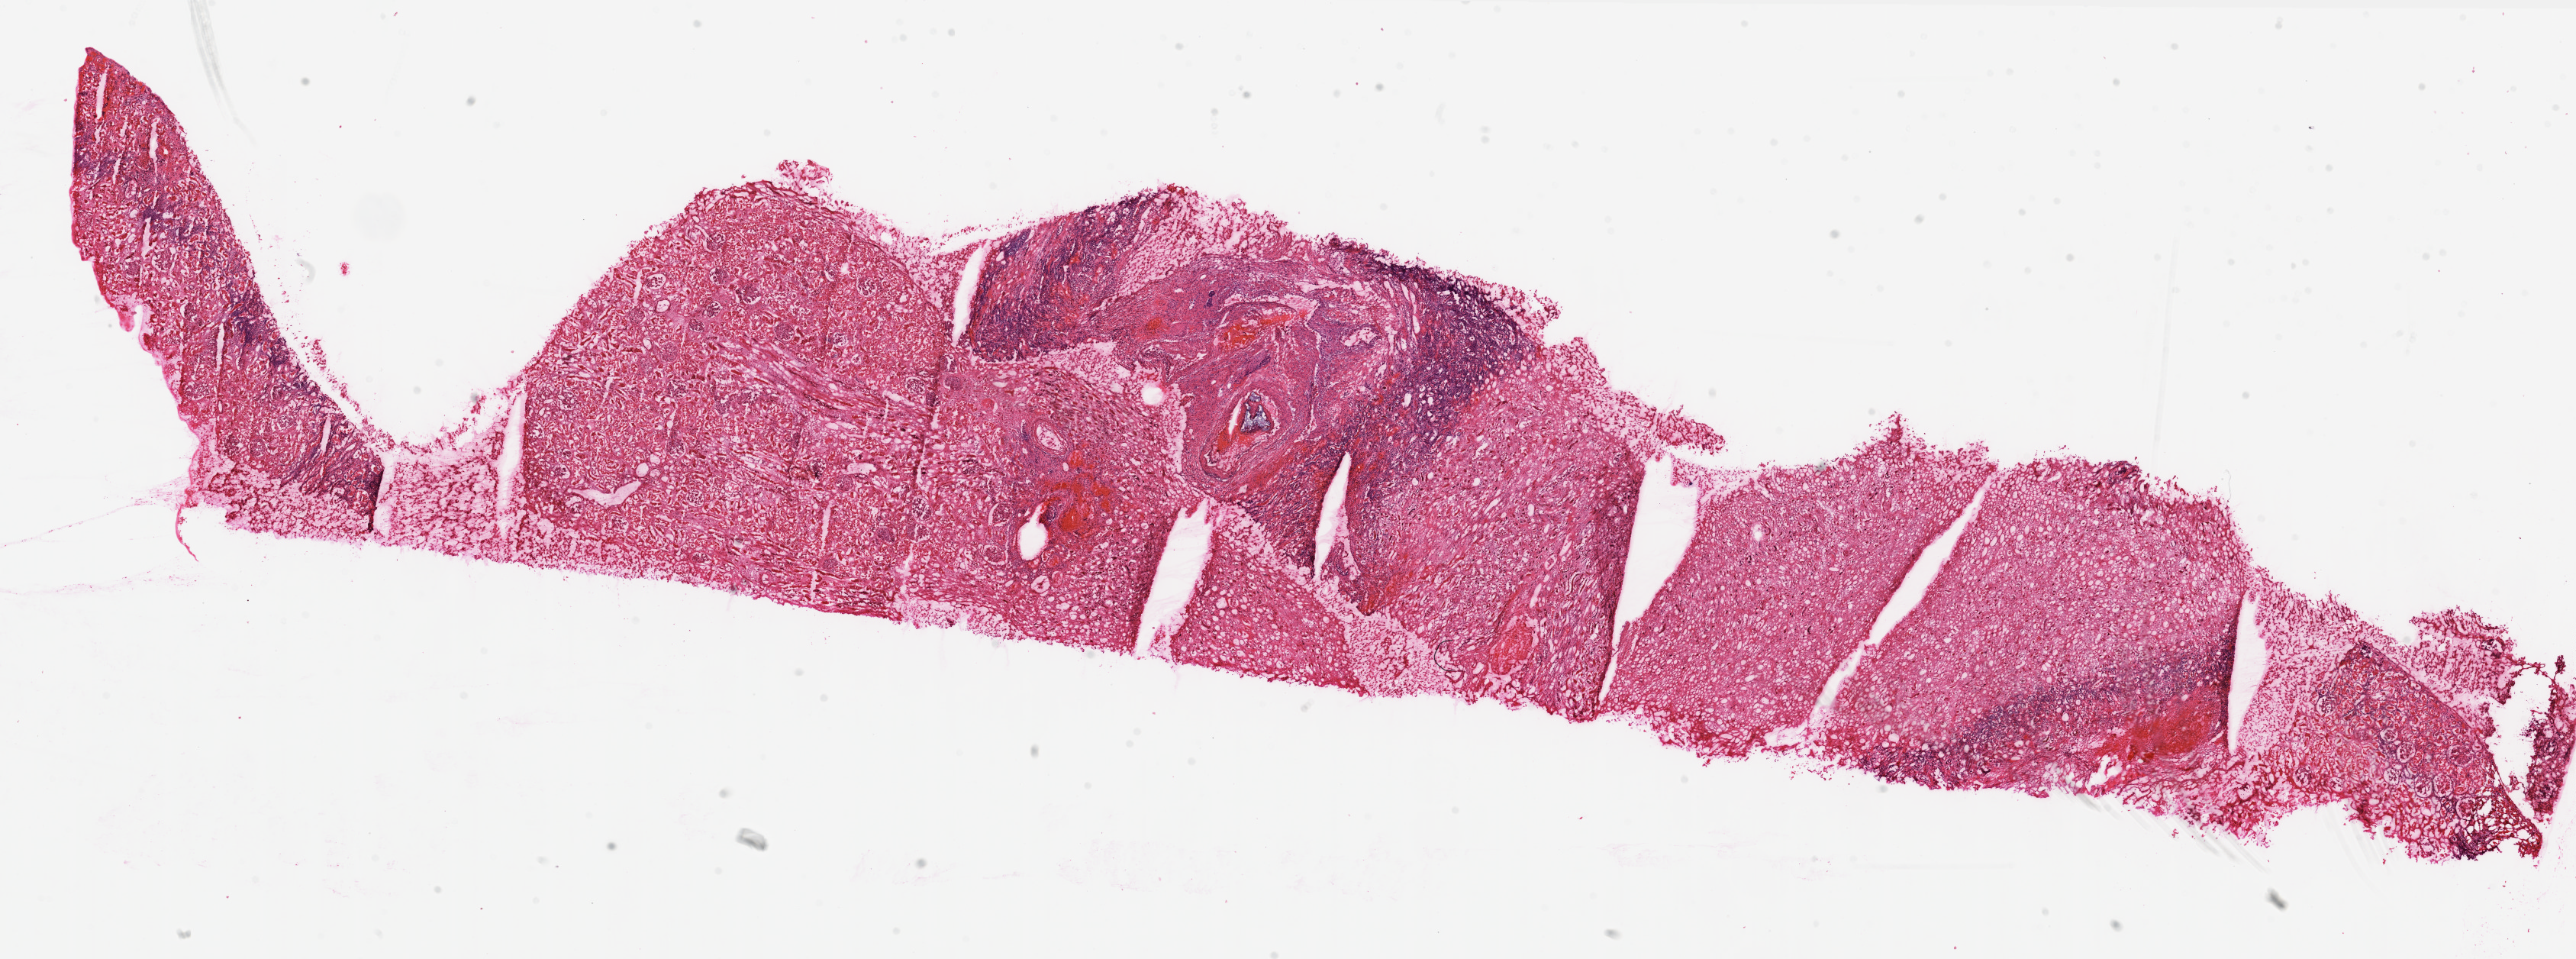
Whole-slide histology image, H&E-stained, low-resolution overview of the scanned area, about 27.1 x 10.1 mm, frozen section from the top of the tissue portion, sample: solid tissue normal (non-tumour tissue), kidney. Patient: female, age at initial diagnosis 57 years.
This section: solid tissue normal sample (biorepository sample class). Patient diagnosis: Clear cell adenocarcinoma, NOS.